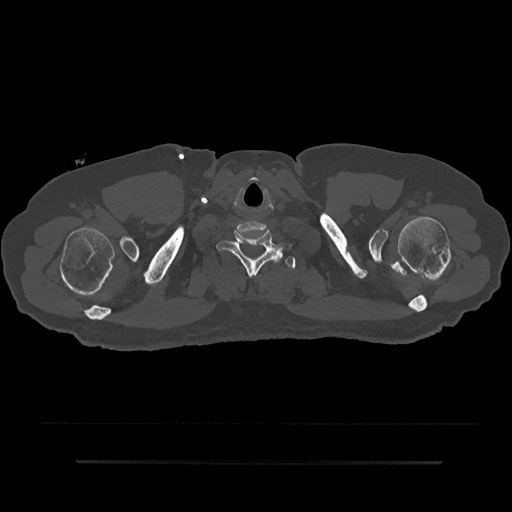
CT including the spine, one axial slice. Position 772 of 797 along the scan axis. Reconstruction kernel Br40s/3. Bone window (W 1800 / L 400 HU). 0.5 mm slice thickness. 512 × 512 image matrix, field of view 464 × 464 mm. Male patient, age 59 years. Case-level facts recorded for this patient, not image findings: primary cancer: bile ducts; vertebrae with lytic lesions (as recorded): T10.
Outlined on this slice (semi-automatic segmentation, software-assisted and operator-edited):
- T1 vertebra: bounding box <274,249,296,269> (left, top, right, bottom; pixels)